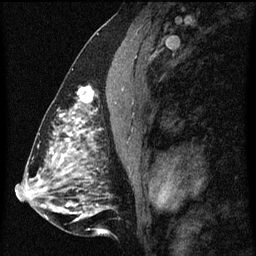
Breast MRI (dynamic contrast-enhanced), one sagittal slice; position 29 of 60 along the scan axis; dynamic contrast-enhanced series, image 2 of 3 at this slice position (ordered by acquisition); 1.5 T; TE 4.2 ms, TR 8 ms; 2 mm slice thickness; 256 × 256 image matrix, field of view 180 × 180 mm. Female patient, age 51 years.
Annotated regions visible in this slice (semi-automatically segmented with operator editing):
- analysis volume of interest (the breast-tissue region the enhancement analysis was run in; not a lesion): bounding box (x1, y1, x2, y2) in pixels: (61, 72, 99, 129)
- tumour enhancement mask (voxels above the 70 % enhancement threshold inside the analysis volume of interest): (61, 86, 95, 129)